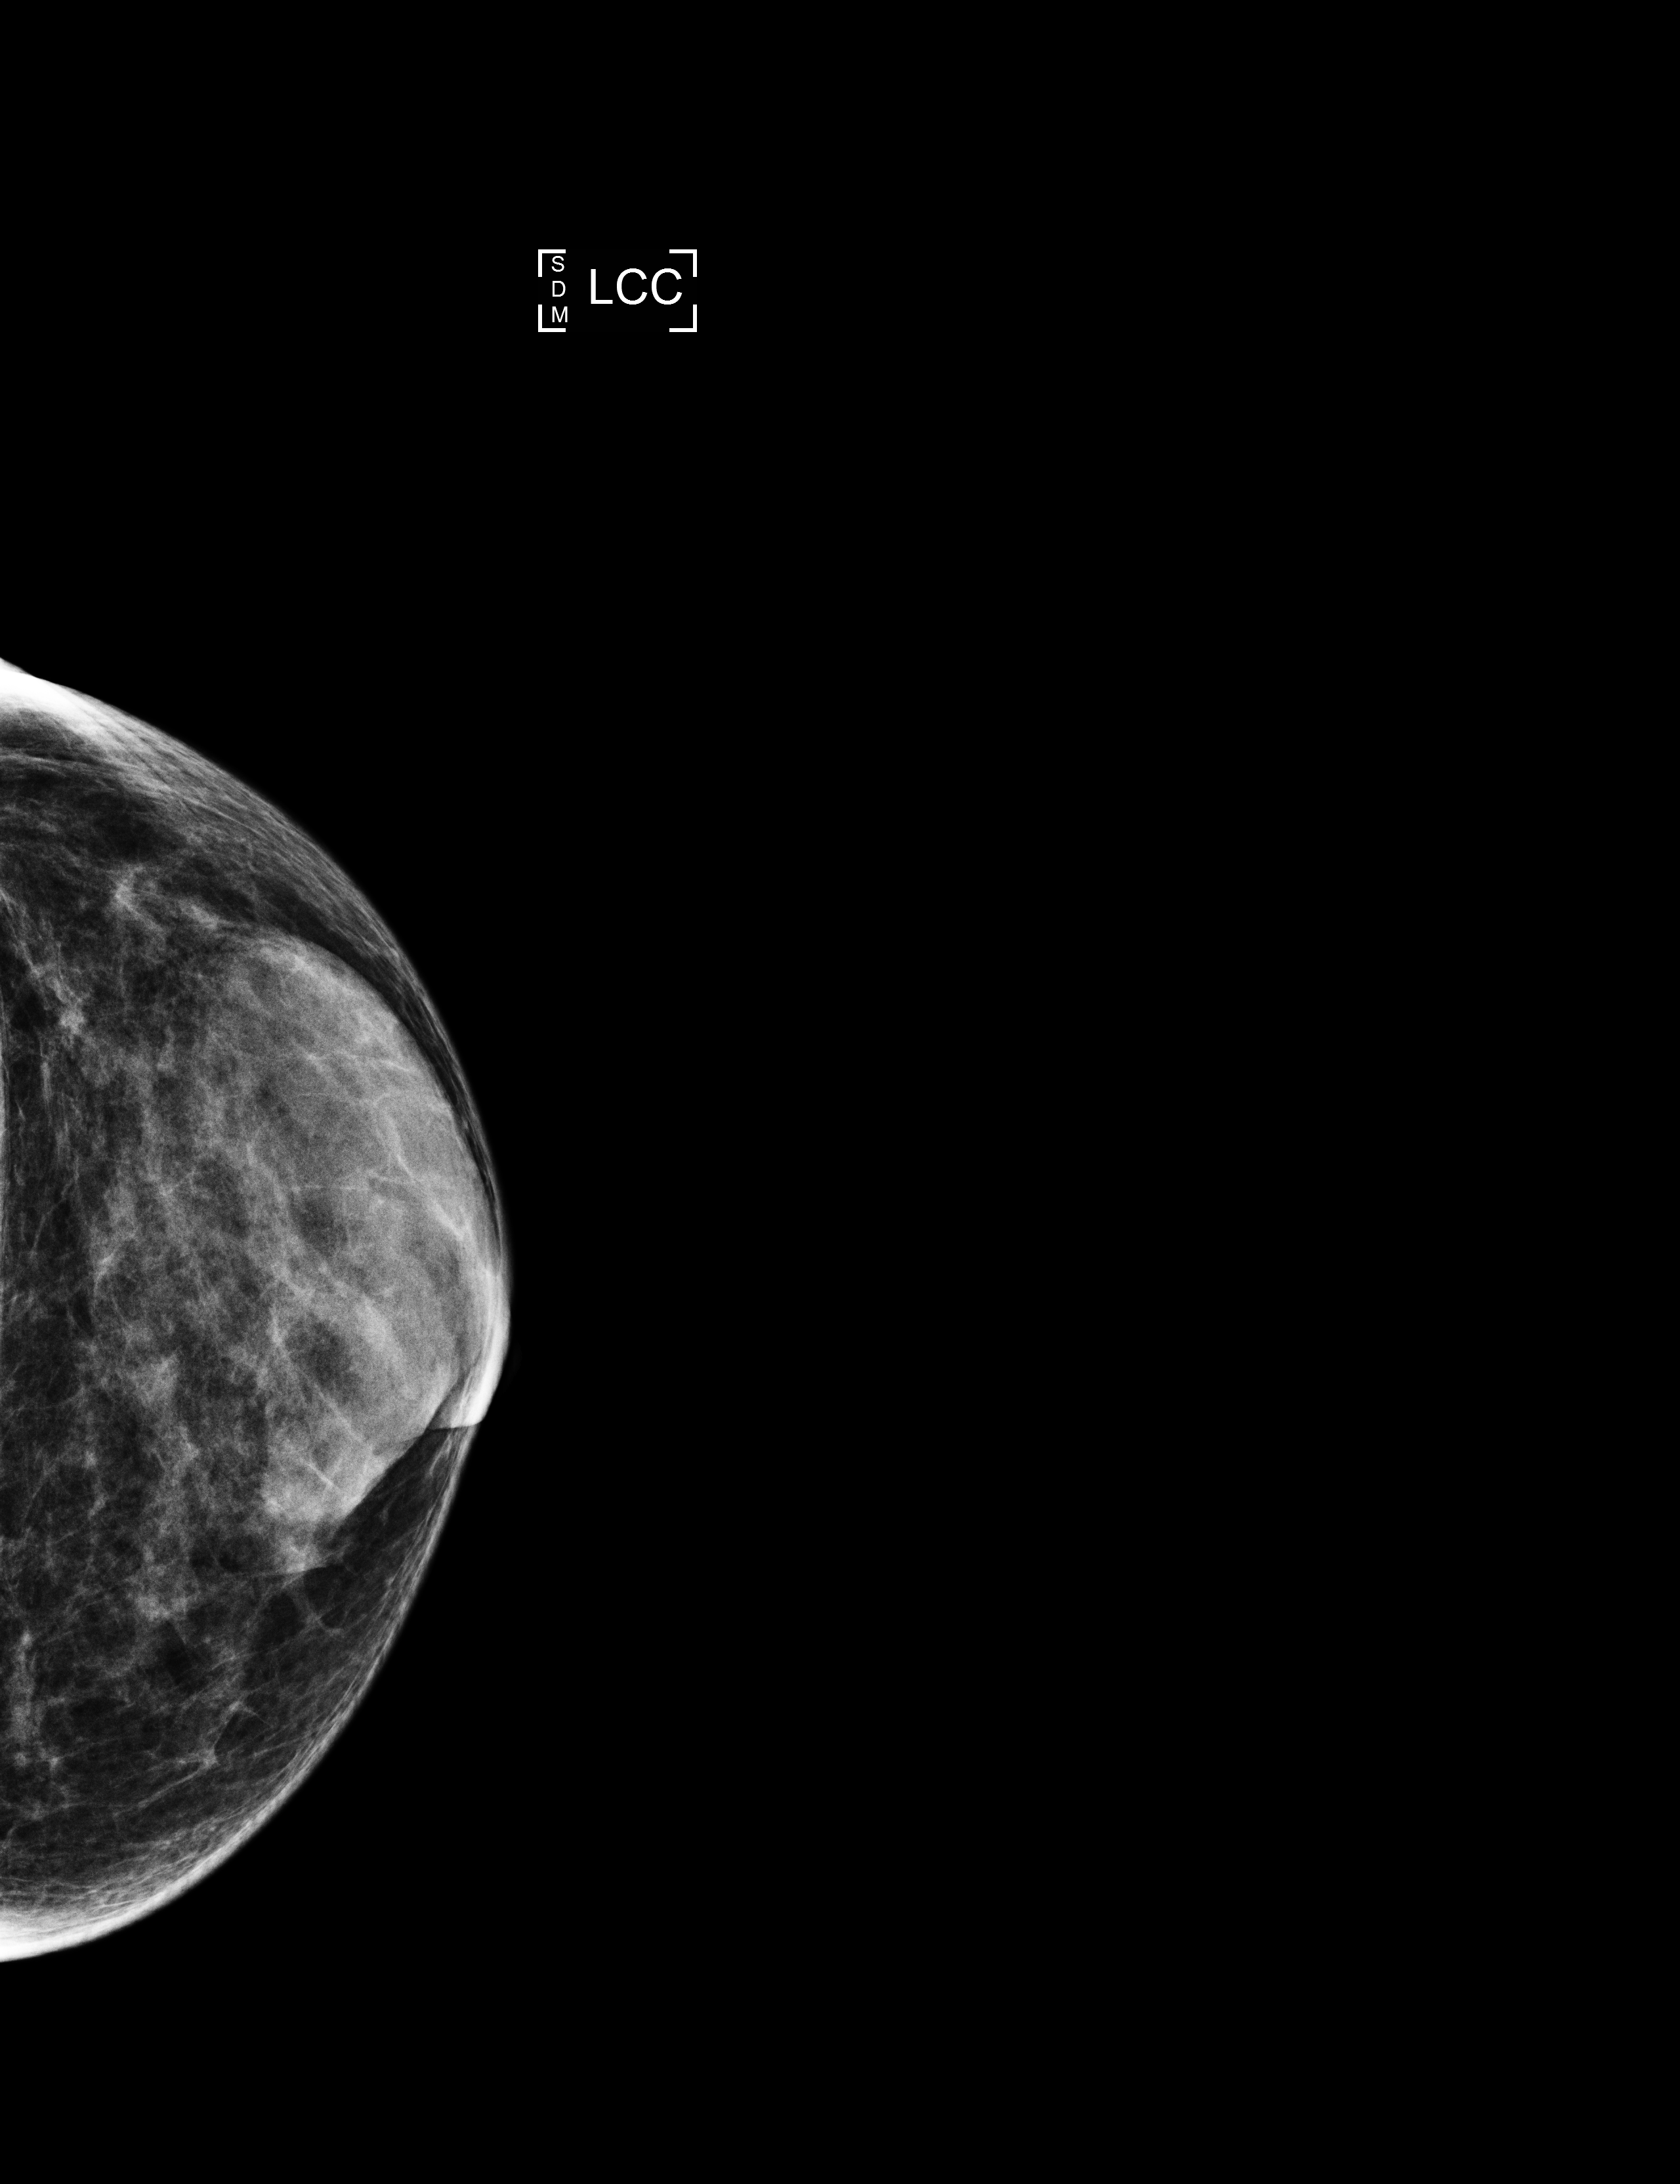
Screening examination. Patient: female, 66 years.
Image type: full-field digital mammogram. Breast: left. Projection: cranio-caudal projection.